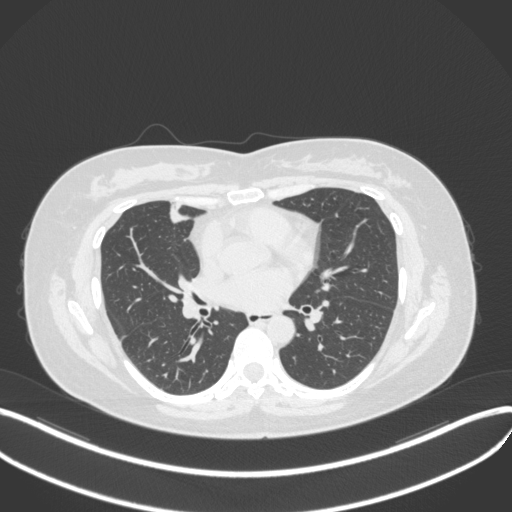
Chest CT, one axial slice; slice 158 of 272 in the series (ordered by position); reconstruction kernel B31f; 120 kVp; lung window (W 1500 / L -600 HU); 1 mm slice thickness; 512 × 512 image matrix, field of view 400 × 400 mm. Female patient, age 42 years. From the clinical record (not read from this slice): clinical TNM (as recorded): T1b N0 M0.
Outlined on this slice (rectangle marked by the reading radiologist):
- lung tumour (recorded histology: adenocarcinoma): box from (x=166, y=200) to (x=192, y=225) px